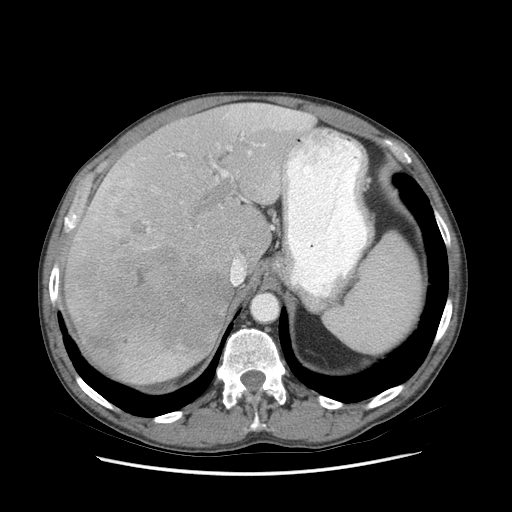
Contrast-enhanced abdominal CT (liver protocol), one axial slice. Slice 57 of 89 in the series (ordered by position). 140 kVp. Soft-tissue window (W 400 / L 40 HU). 2.5 mm slice thickness. 512 × 512 image matrix, field of view 380 × 380 mm. Case-level facts recorded for this patient, not image findings: diagnosis: hepatocellular carcinoma (patient treated with transarterial chemoembolisation; whether this scan precedes or follows treatment is not stated here); TNM stage (as recorded): Stage-IIIB; Child-Pugh class: A; tumour differentiation: moderately differentiated; tumour nodularity: multinodular.
Structures marked on this image (semi-automatic segmentation, software-assisted and operator-edited):
- liver parenchyma outside the tumour (the mass and vessels are separate outlines, so this box may not span the whole liver): bounding box (x1, y1, x2, y2) in pixels: (64, 102, 312, 384)
- mass: (67, 214, 227, 372)
- liver vessels: (94, 104, 309, 270)